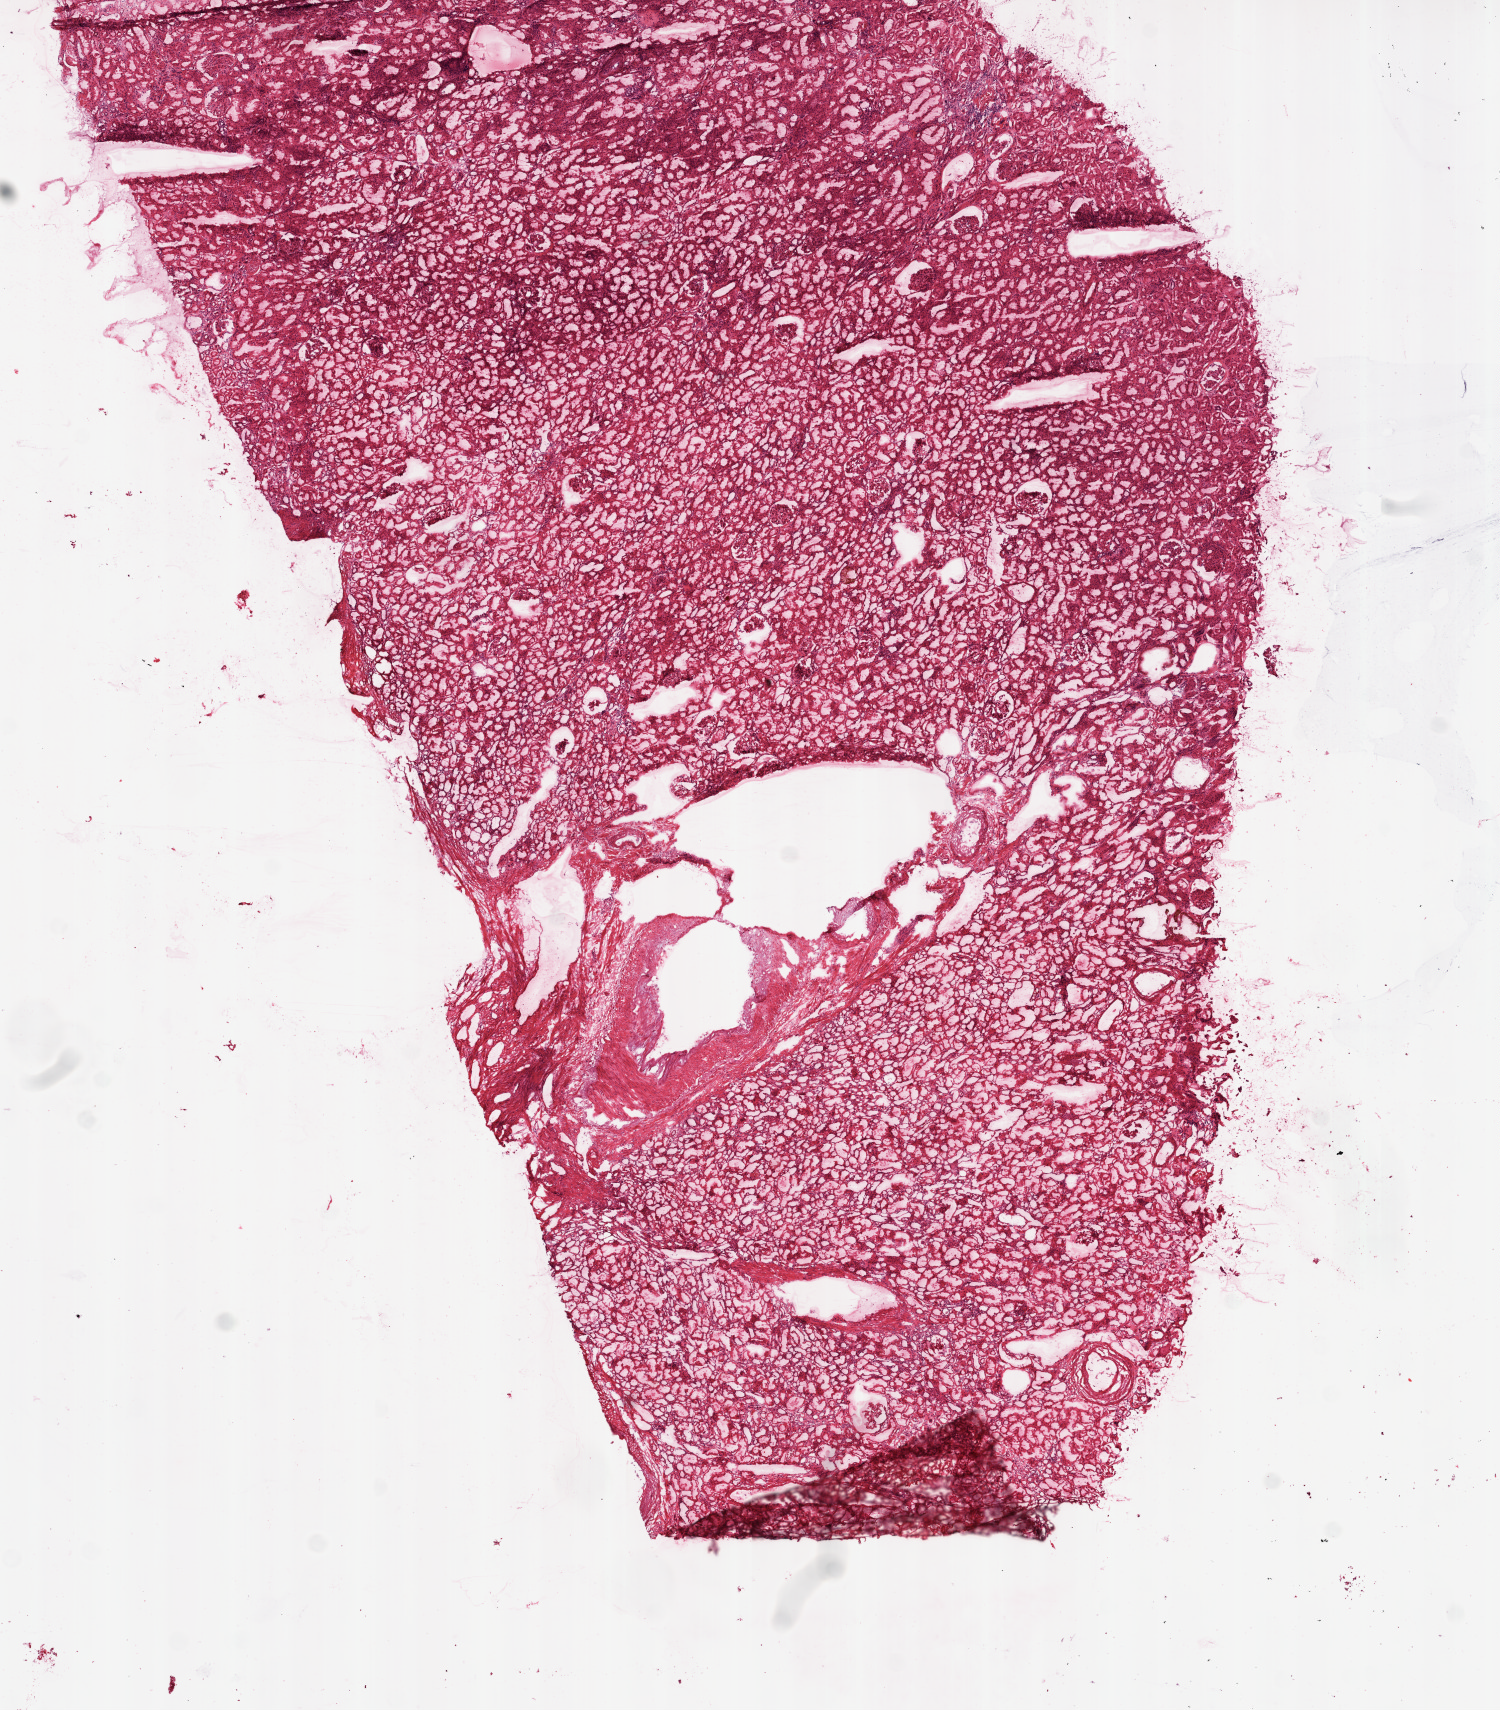
H&E-stained whole-slide image, low-resolution overview of the scanned area, about 12.0 x 13.7 mm (acquisition: 20x scan), frozen section from the top of the tissue portion, kidney, solid tissue normal (non-tumour tissue) sample. Patient: female, age at initial diagnosis 49 years.
This section: solid tissue normal sample (biorepository sample class). Patient diagnosis: Clear cell adenocarcinoma, NOS.